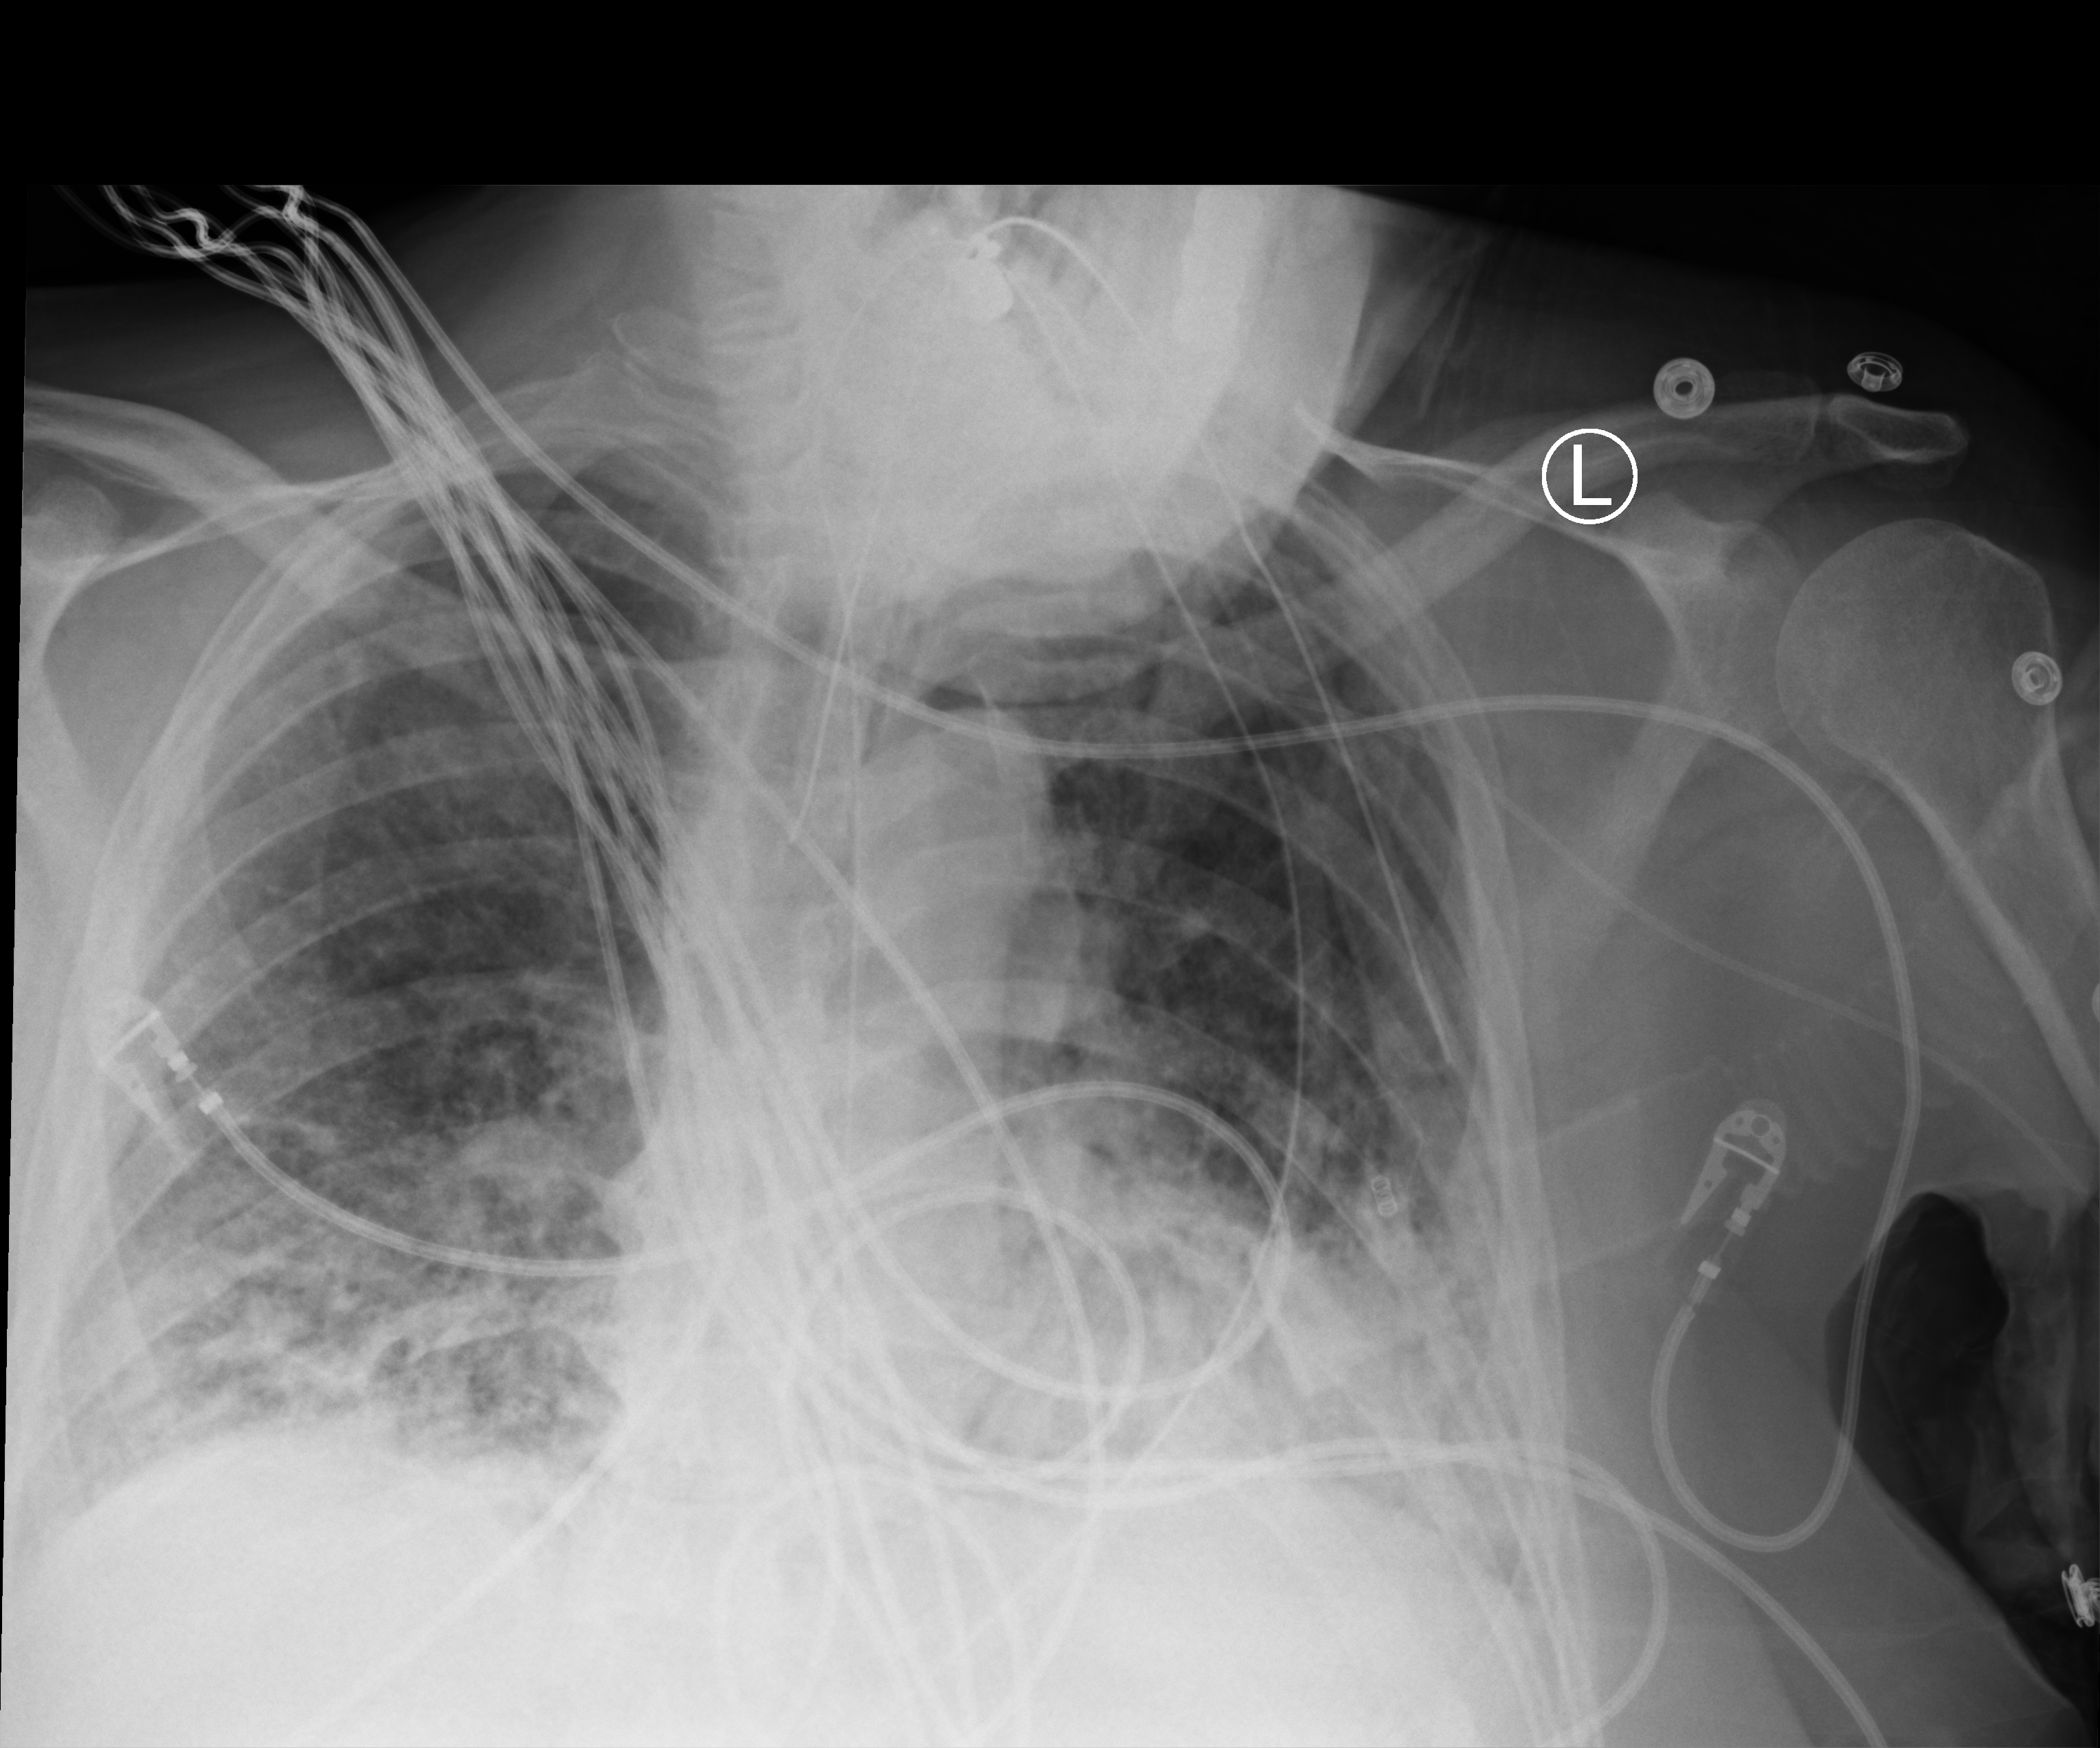
Portable chest radiograph, anteroposterior (AP) projection. Male patient hospitalised with COVID-19, age 60–74 years.
Admission-level facts for this patient (not findings on this image; timing relative to this image not recorded):
- length of hospital stay: 40 days